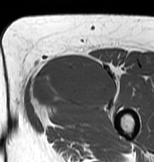
MRI of an extremity soft-tissue mass, one axial slice; slice 34 of 83 in the series (ordered by position); MR volume resampled by the dataset authors to the PET/CT grid (not the native acquisition matrix); 154 × 162 image matrix, field of view 150 × 158 mm. Female patient. From the clinical record (not read from this slice): histological type: myxofibrosarcoma; grade: intermediate; site of the primary tumour: left thigh.
Outlined on this slice (expert contour drawn on MRI and transferred to this co-registered scan by the dataset authors):
- gross tumour volume including surrounding oedema: bounding box [x1, y1, x2, y2] px = [28, 52, 120, 126]
- gross tumour volume (mass): [30, 52, 116, 110]